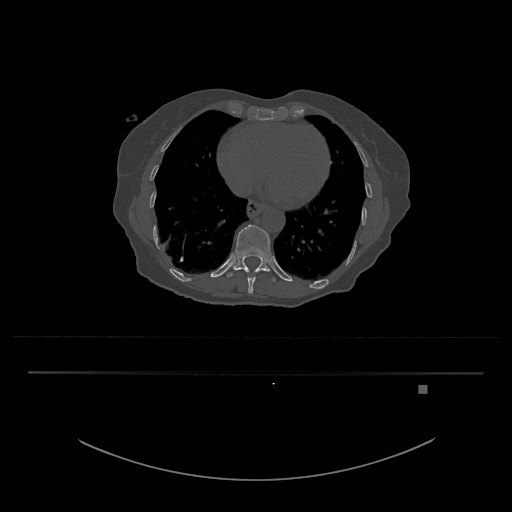
CT including the spine, one axial slice; position 683 of 797 along the scan axis; reconstruction kernel Br40s/3; 120 kVp; bone window (W 1800 / L 400 HU); 0.5 mm slice thickness; 512 × 512 image matrix, field of view 500 × 500 mm. Patient: female, 57 years. From the clinical record (not read from this slice): primary cancer: cervical.
Structures marked on this image (semi-automatically segmented with operator editing):
- T10 vertebra: bounding box <244,270,260,294> (left, top, right, bottom; pixels)
- T11 vertebra: <226,225,276,282>